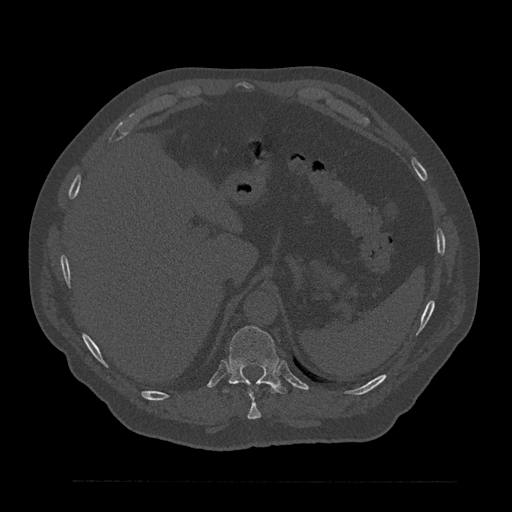
CT including the spine, one axial slice; position 313 of 797 along the scan axis; reconstruction kernel Br40s/3; 120 kVp; bone window (W 1800 / L 400 HU); 0.5 mm slice thickness; 512 × 512 image matrix, field of view 430 × 430 mm. Male patient, age 61 years. From the clinical record (not read from this slice): primary cancer: prostate.
Annotated regions visible in this slice (semi-automatically segmented with operator editing):
- T10 vertebra: bounding box <247,390,262,420> (left, top, right, bottom; pixels)
- T11 vertebra: <229,326,288,394>